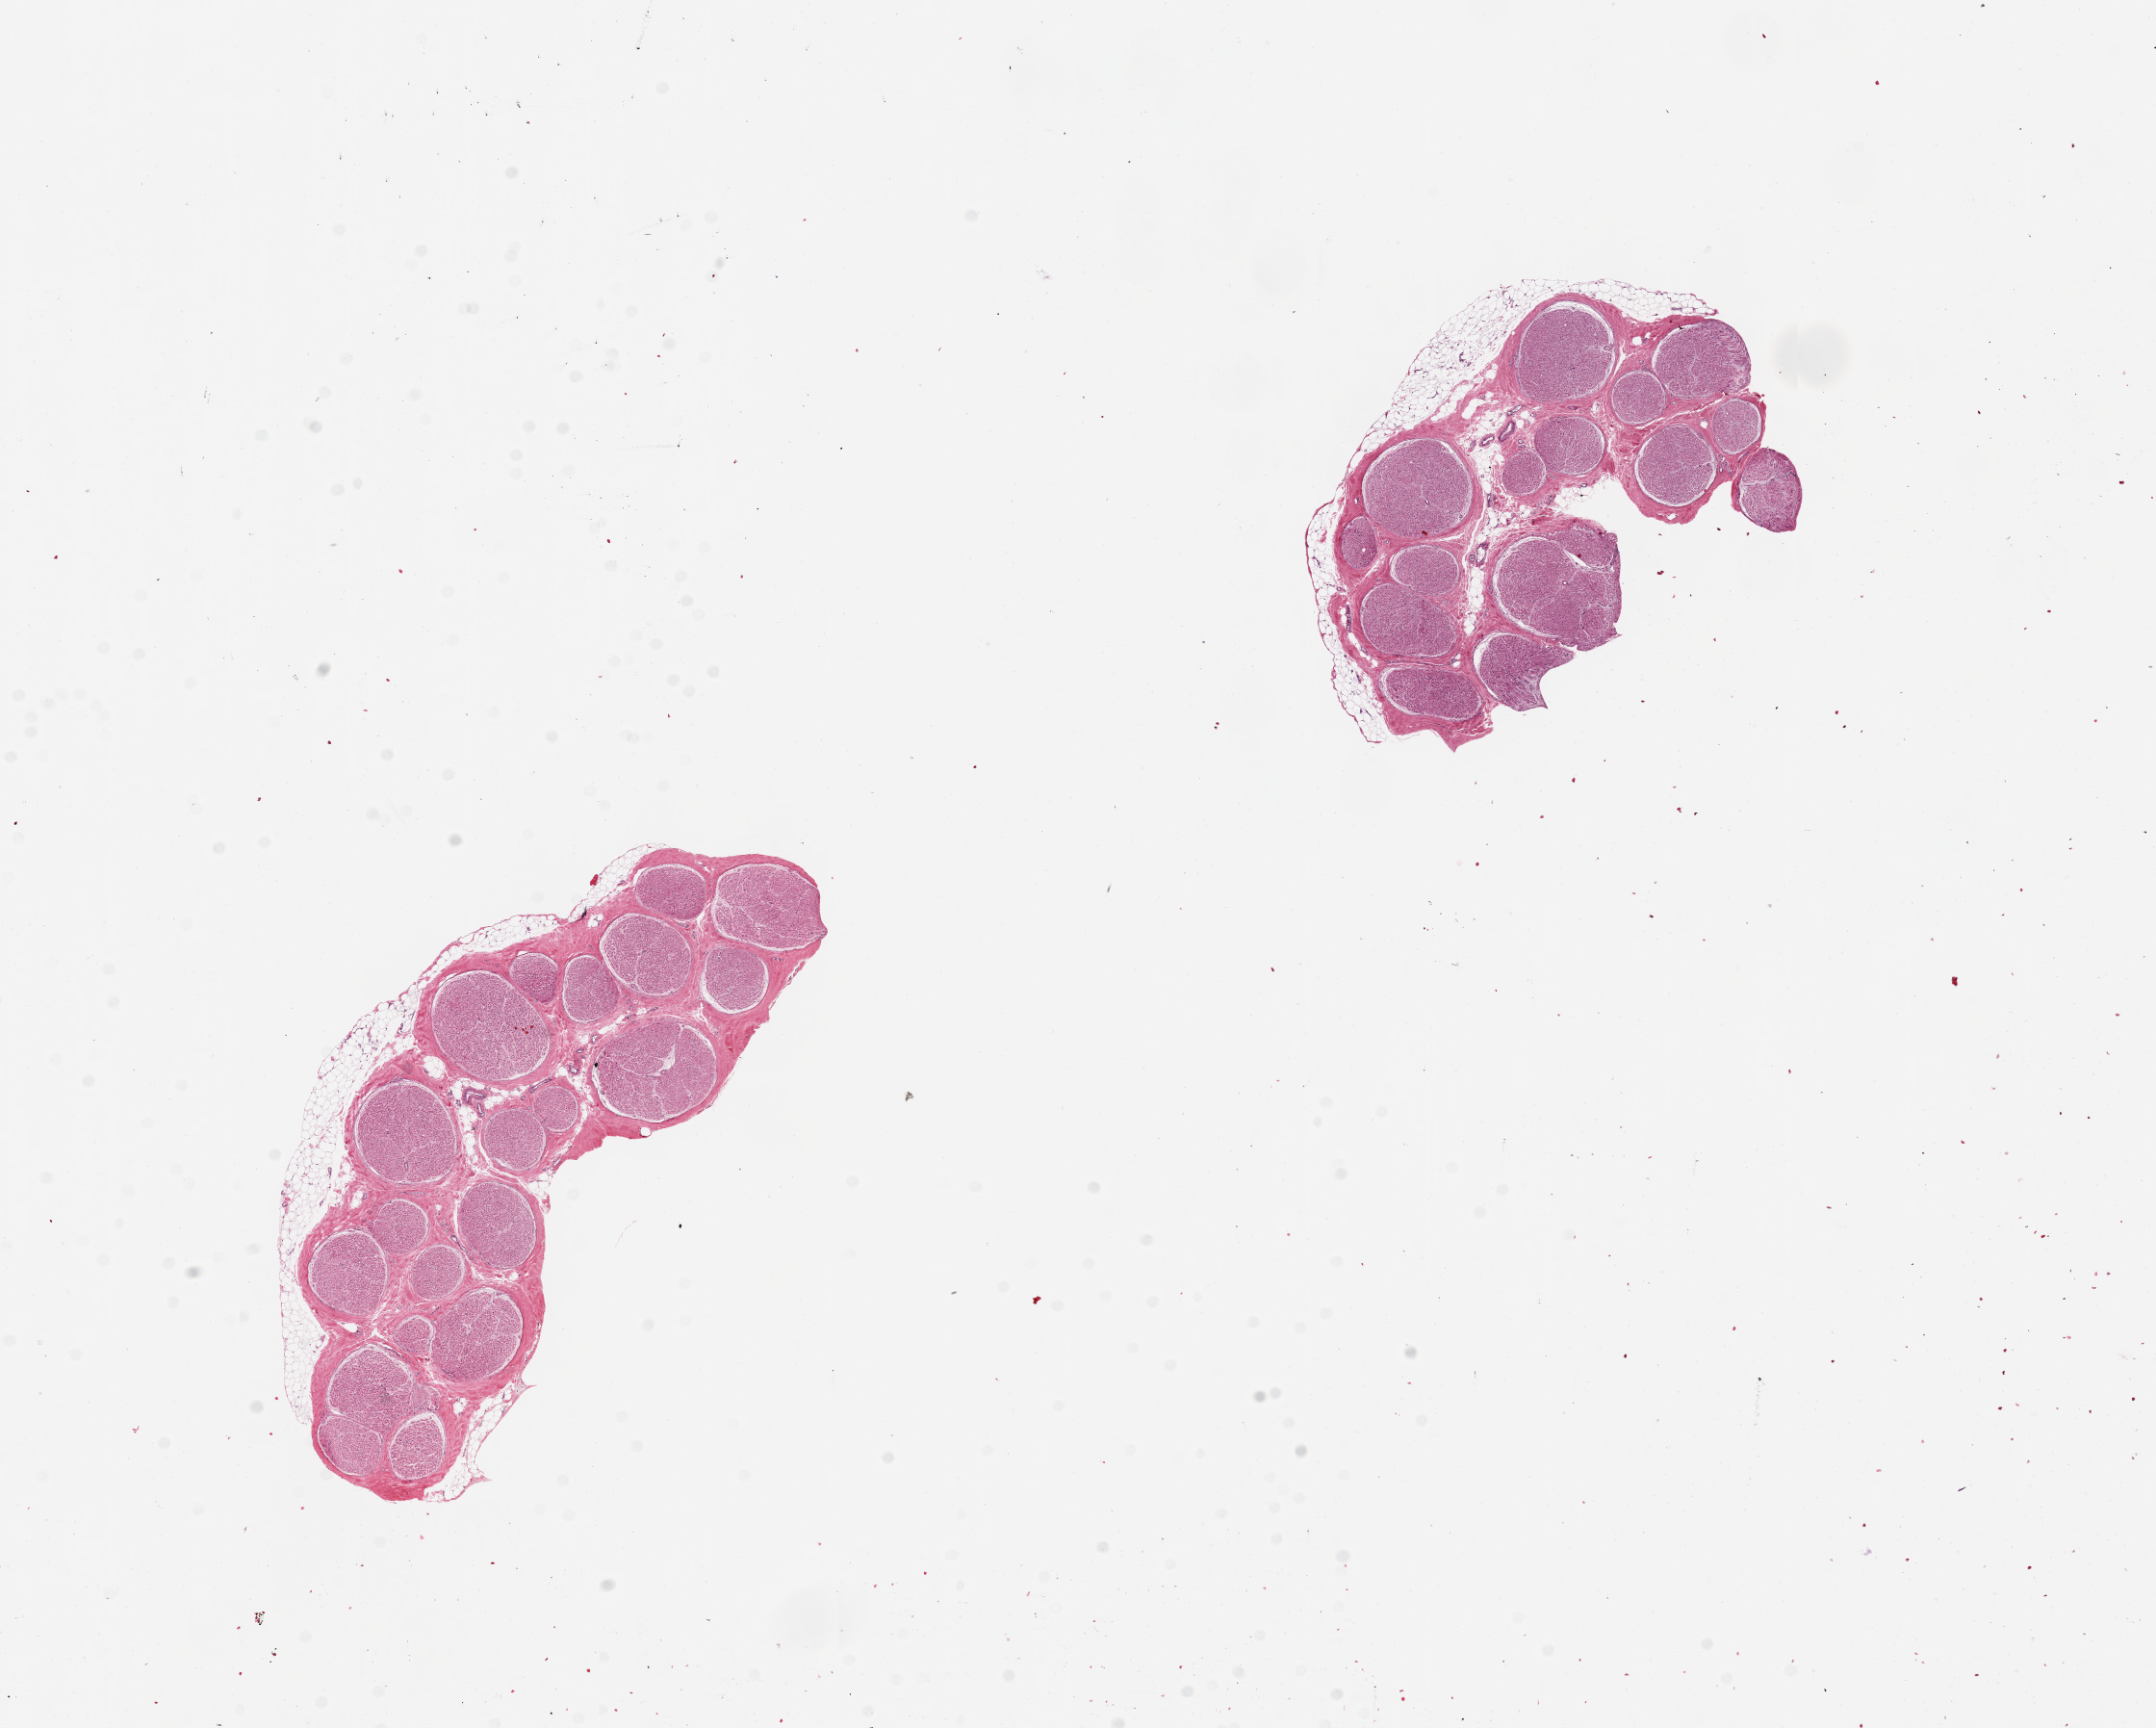
Haematoxylin and eosin whole-slide image, a low-resolution overview of the entire scanned area, about 17.7 x 14.2 mm (from a 20x scan), PAXgene-fixed, paraffin-embedded tissue, section of tibial nerve (target tissue), donor tissue sample. Donor sex: female.
• pathologist's review note for this sample: 2 pieces, 6x3 & 4.5x3mm; 10% external adipose